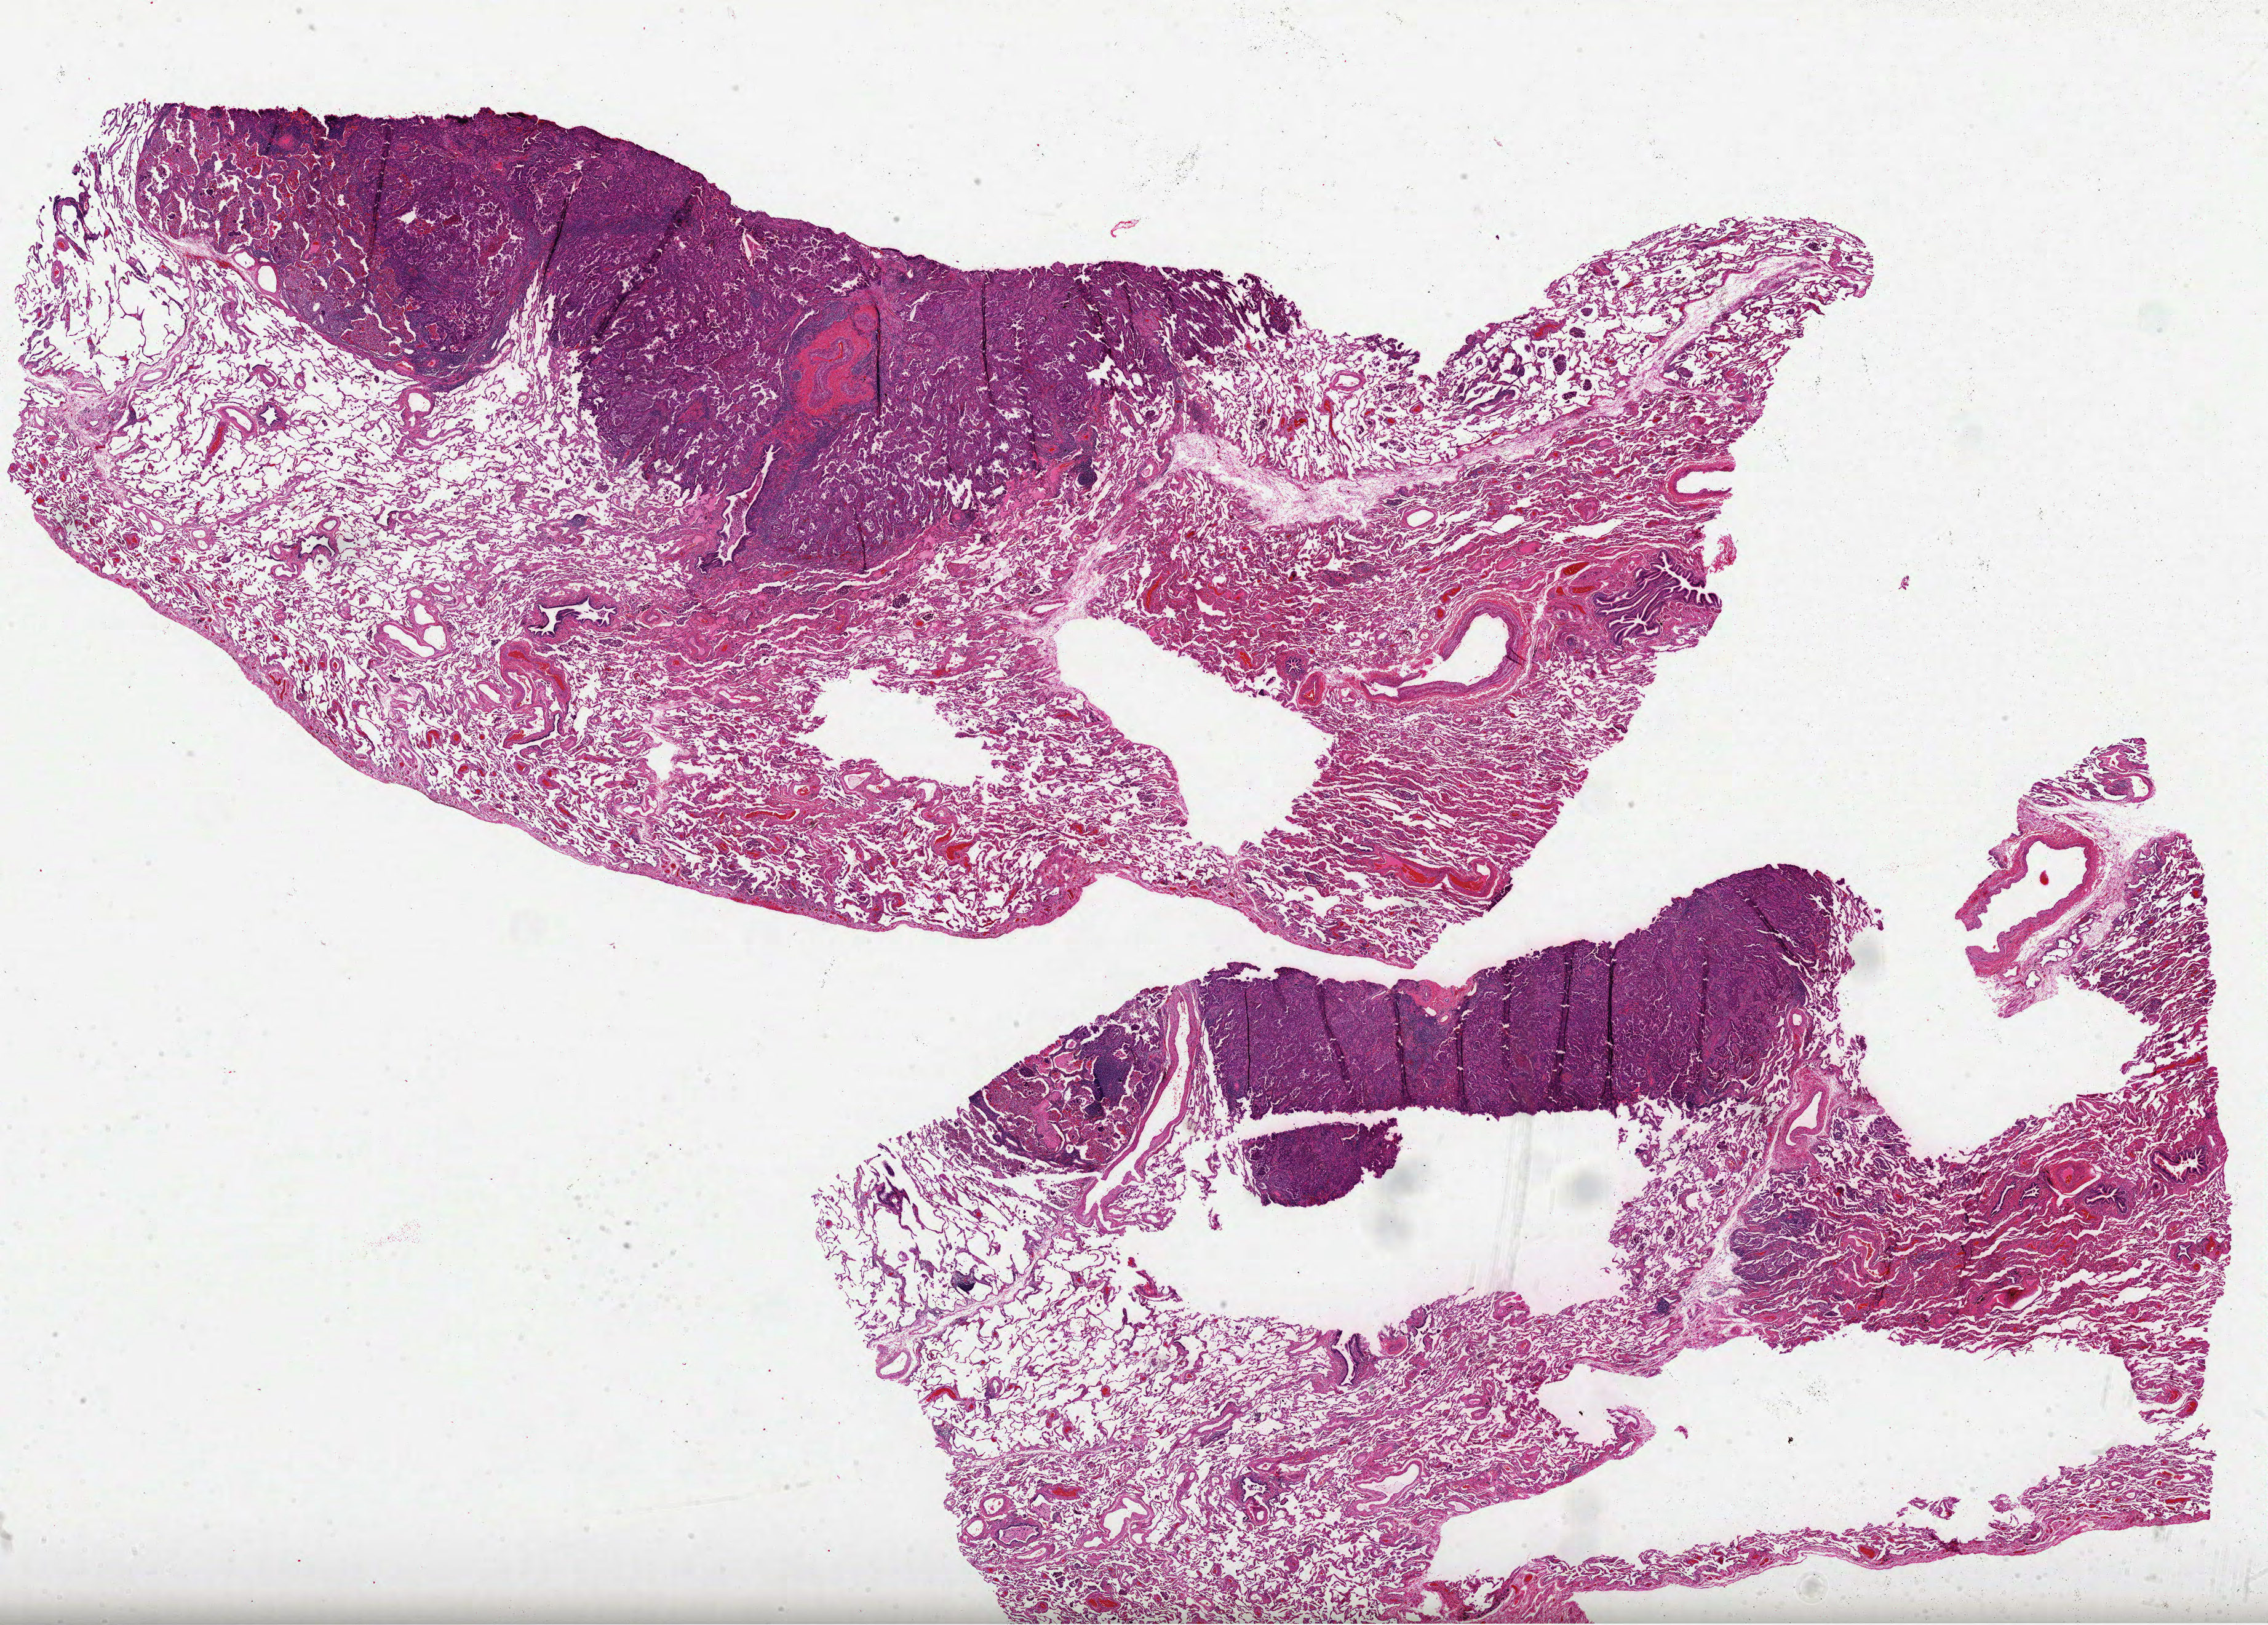
Whole-slide histology image, Hematoxylin and eosin (H&E) stained, shown as a low-resolution overview of the whole scanned area (about 29.7 x 21.3 mm, slide scanned at 40x). FFPE section. Primary tumour sample from the lung. Patient: female, age at initial diagnosis 74 years.
Laterality: left. Histologic diagnosis: Adenocarcinoma, NOS (lower lobe, lung). AJCC pathologic stage: IA.